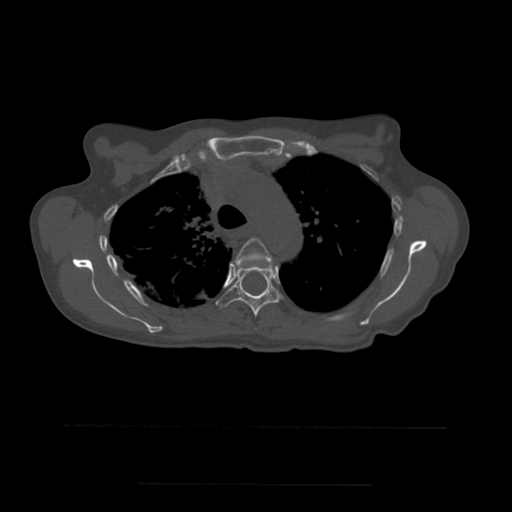
CT including the spine, one axial slice; position 396 of 544 along the scan axis; bone window (W 1800 / L 400 HU); 1.25 mm slice thickness; 512 × 512 image matrix. Patient age 58 years. Case-level facts recorded for this patient, not image findings: primary cancer: lung.
Annotated regions visible in this slice (semi-automatically segmented with operator editing):
- T4 vertebra: bounding box (x1, y1, x2, y2) in pixels: (235, 238, 273, 269)
- T5 vertebra: (216, 260, 282, 317)